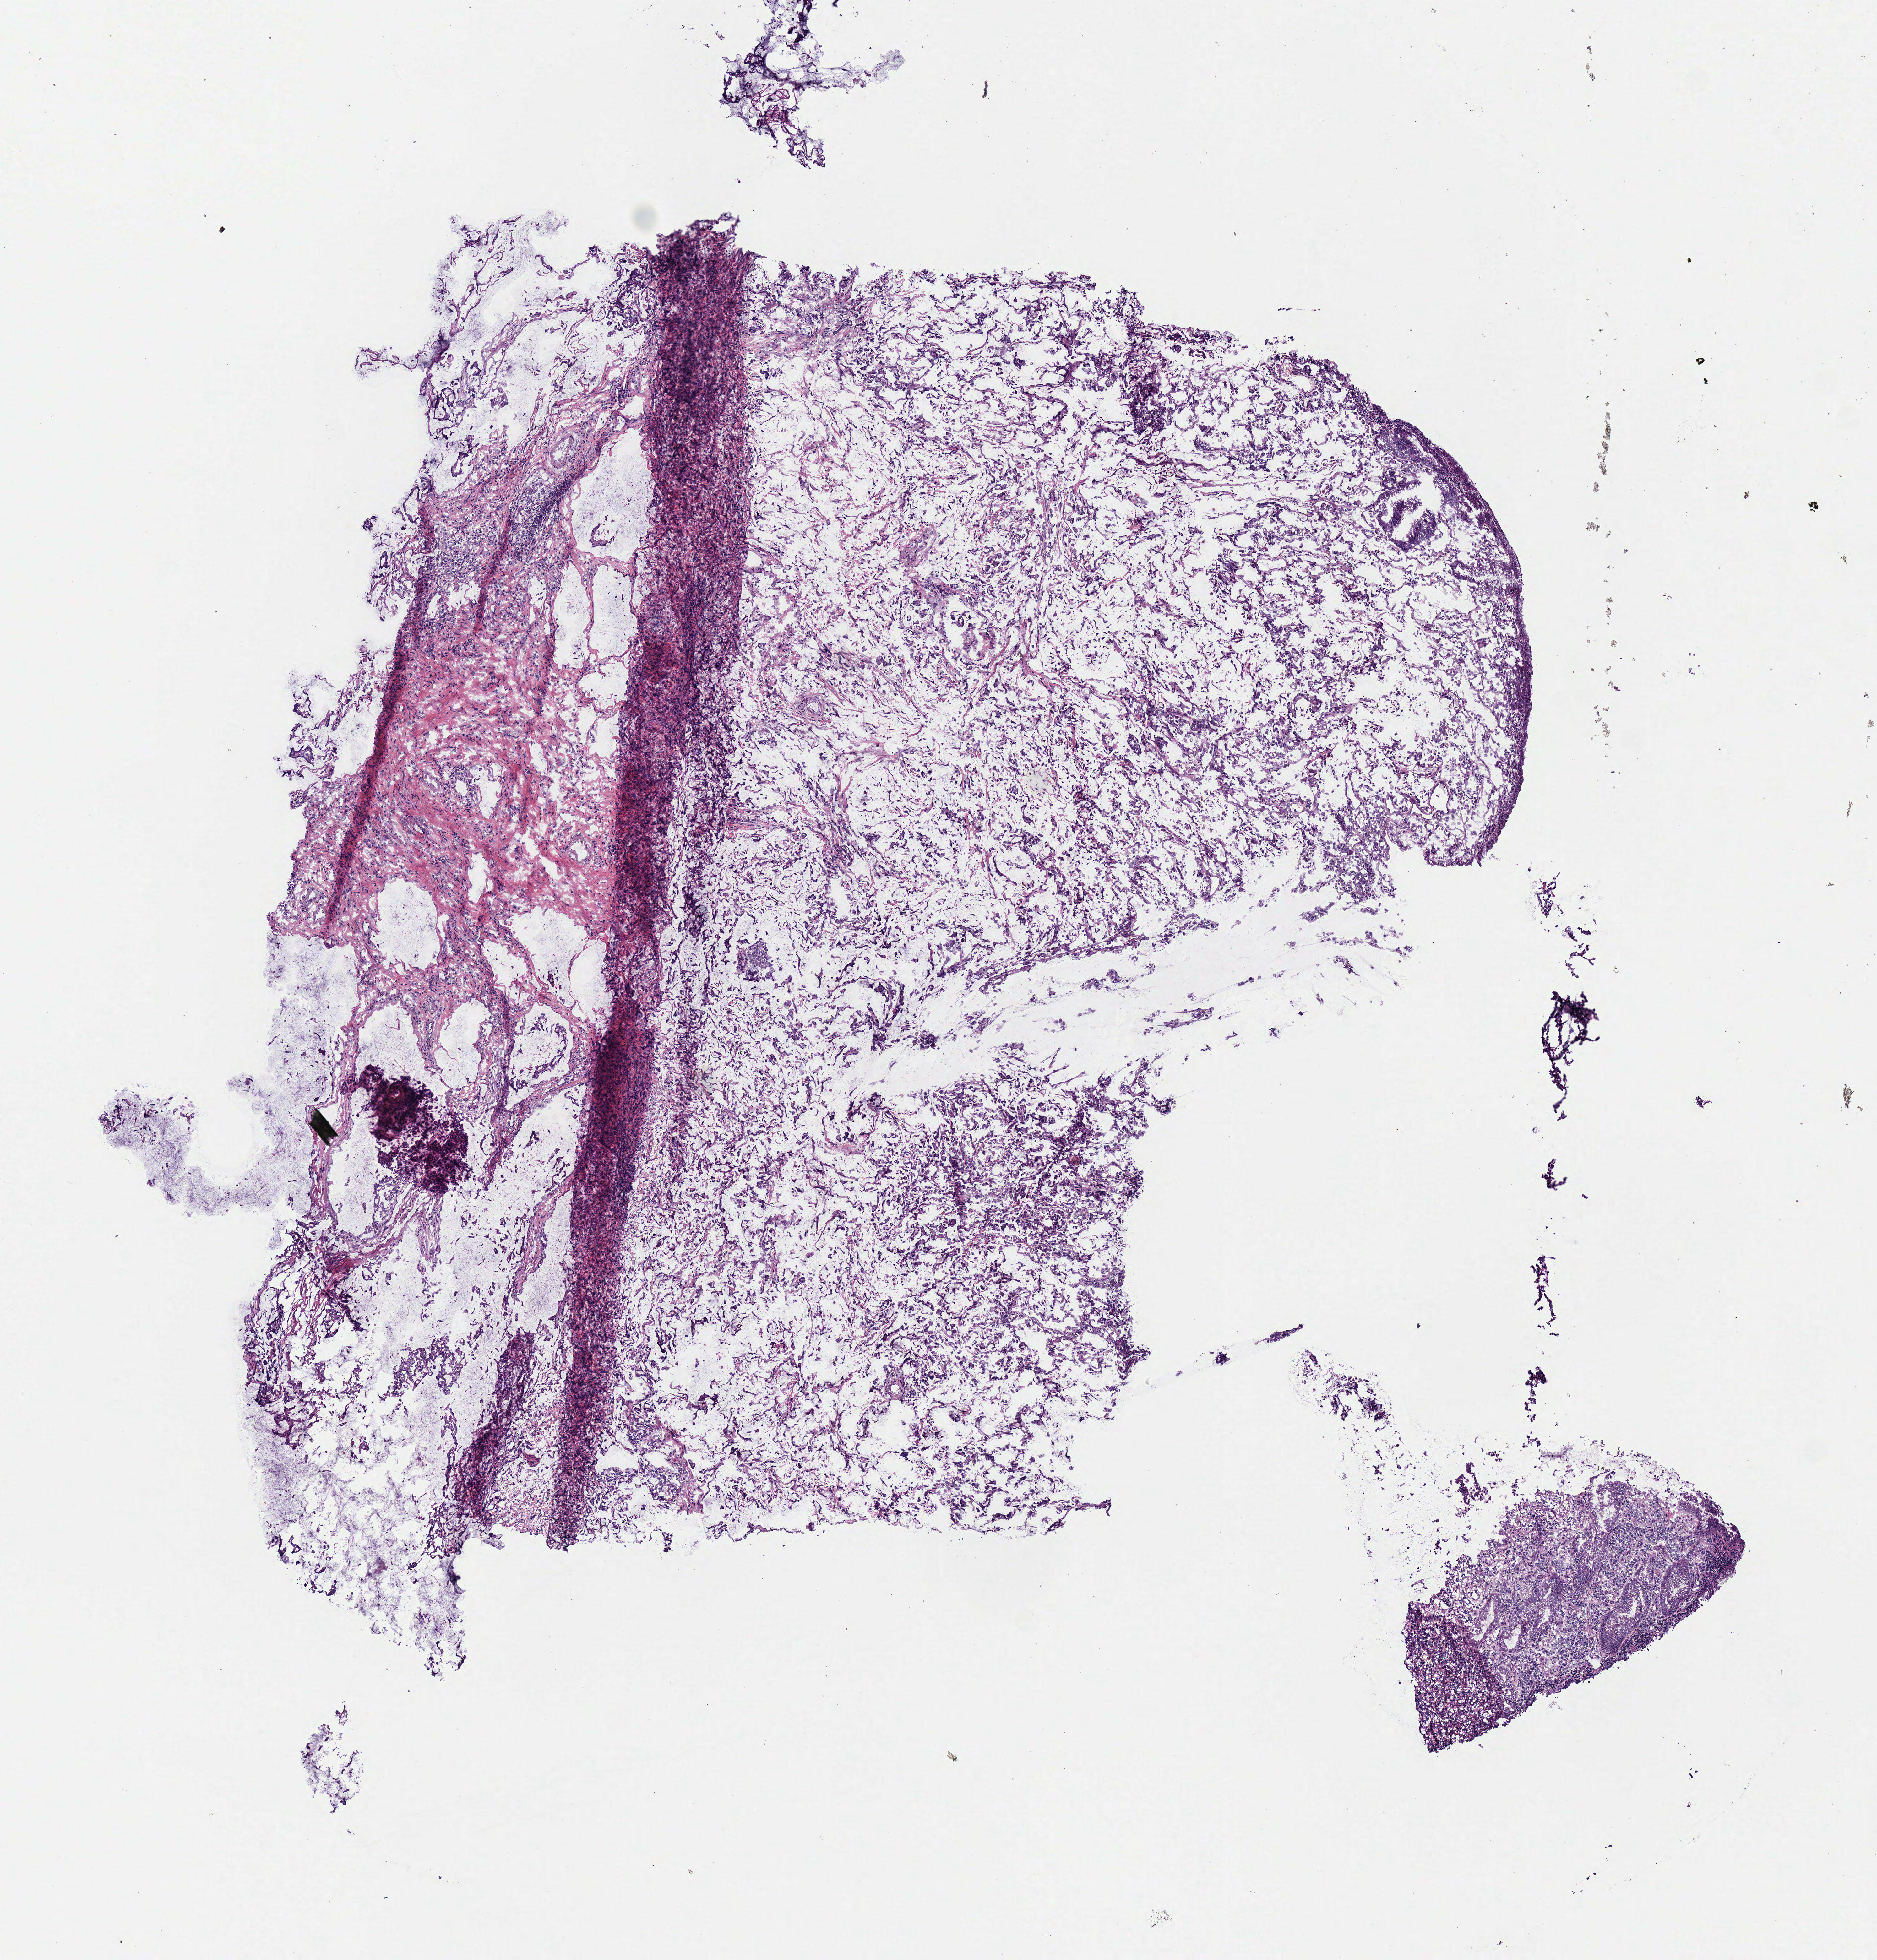
Whole-slide histology image, Hematoxylin and eosin (H&E) stained — shown as a low-resolution overview of the whole scanned area (about 5.9 x 6.1 mm), frozen section from the bottom of the tissue portion, primary tumour sample from the stomach. Male, age 58 years at initial diagnosis. Histologic grade: G3 (poorly differentiated). Composition of this section per pathologist review: tumour cells 75%, tumour nuclei 75%, normal cells 5%, stromal cells 25%, necrosis 0%.
AJCC pathologic stage: IB (6th edition). Diagnosis: Carcinoma, diffuse type (gastric antrum).